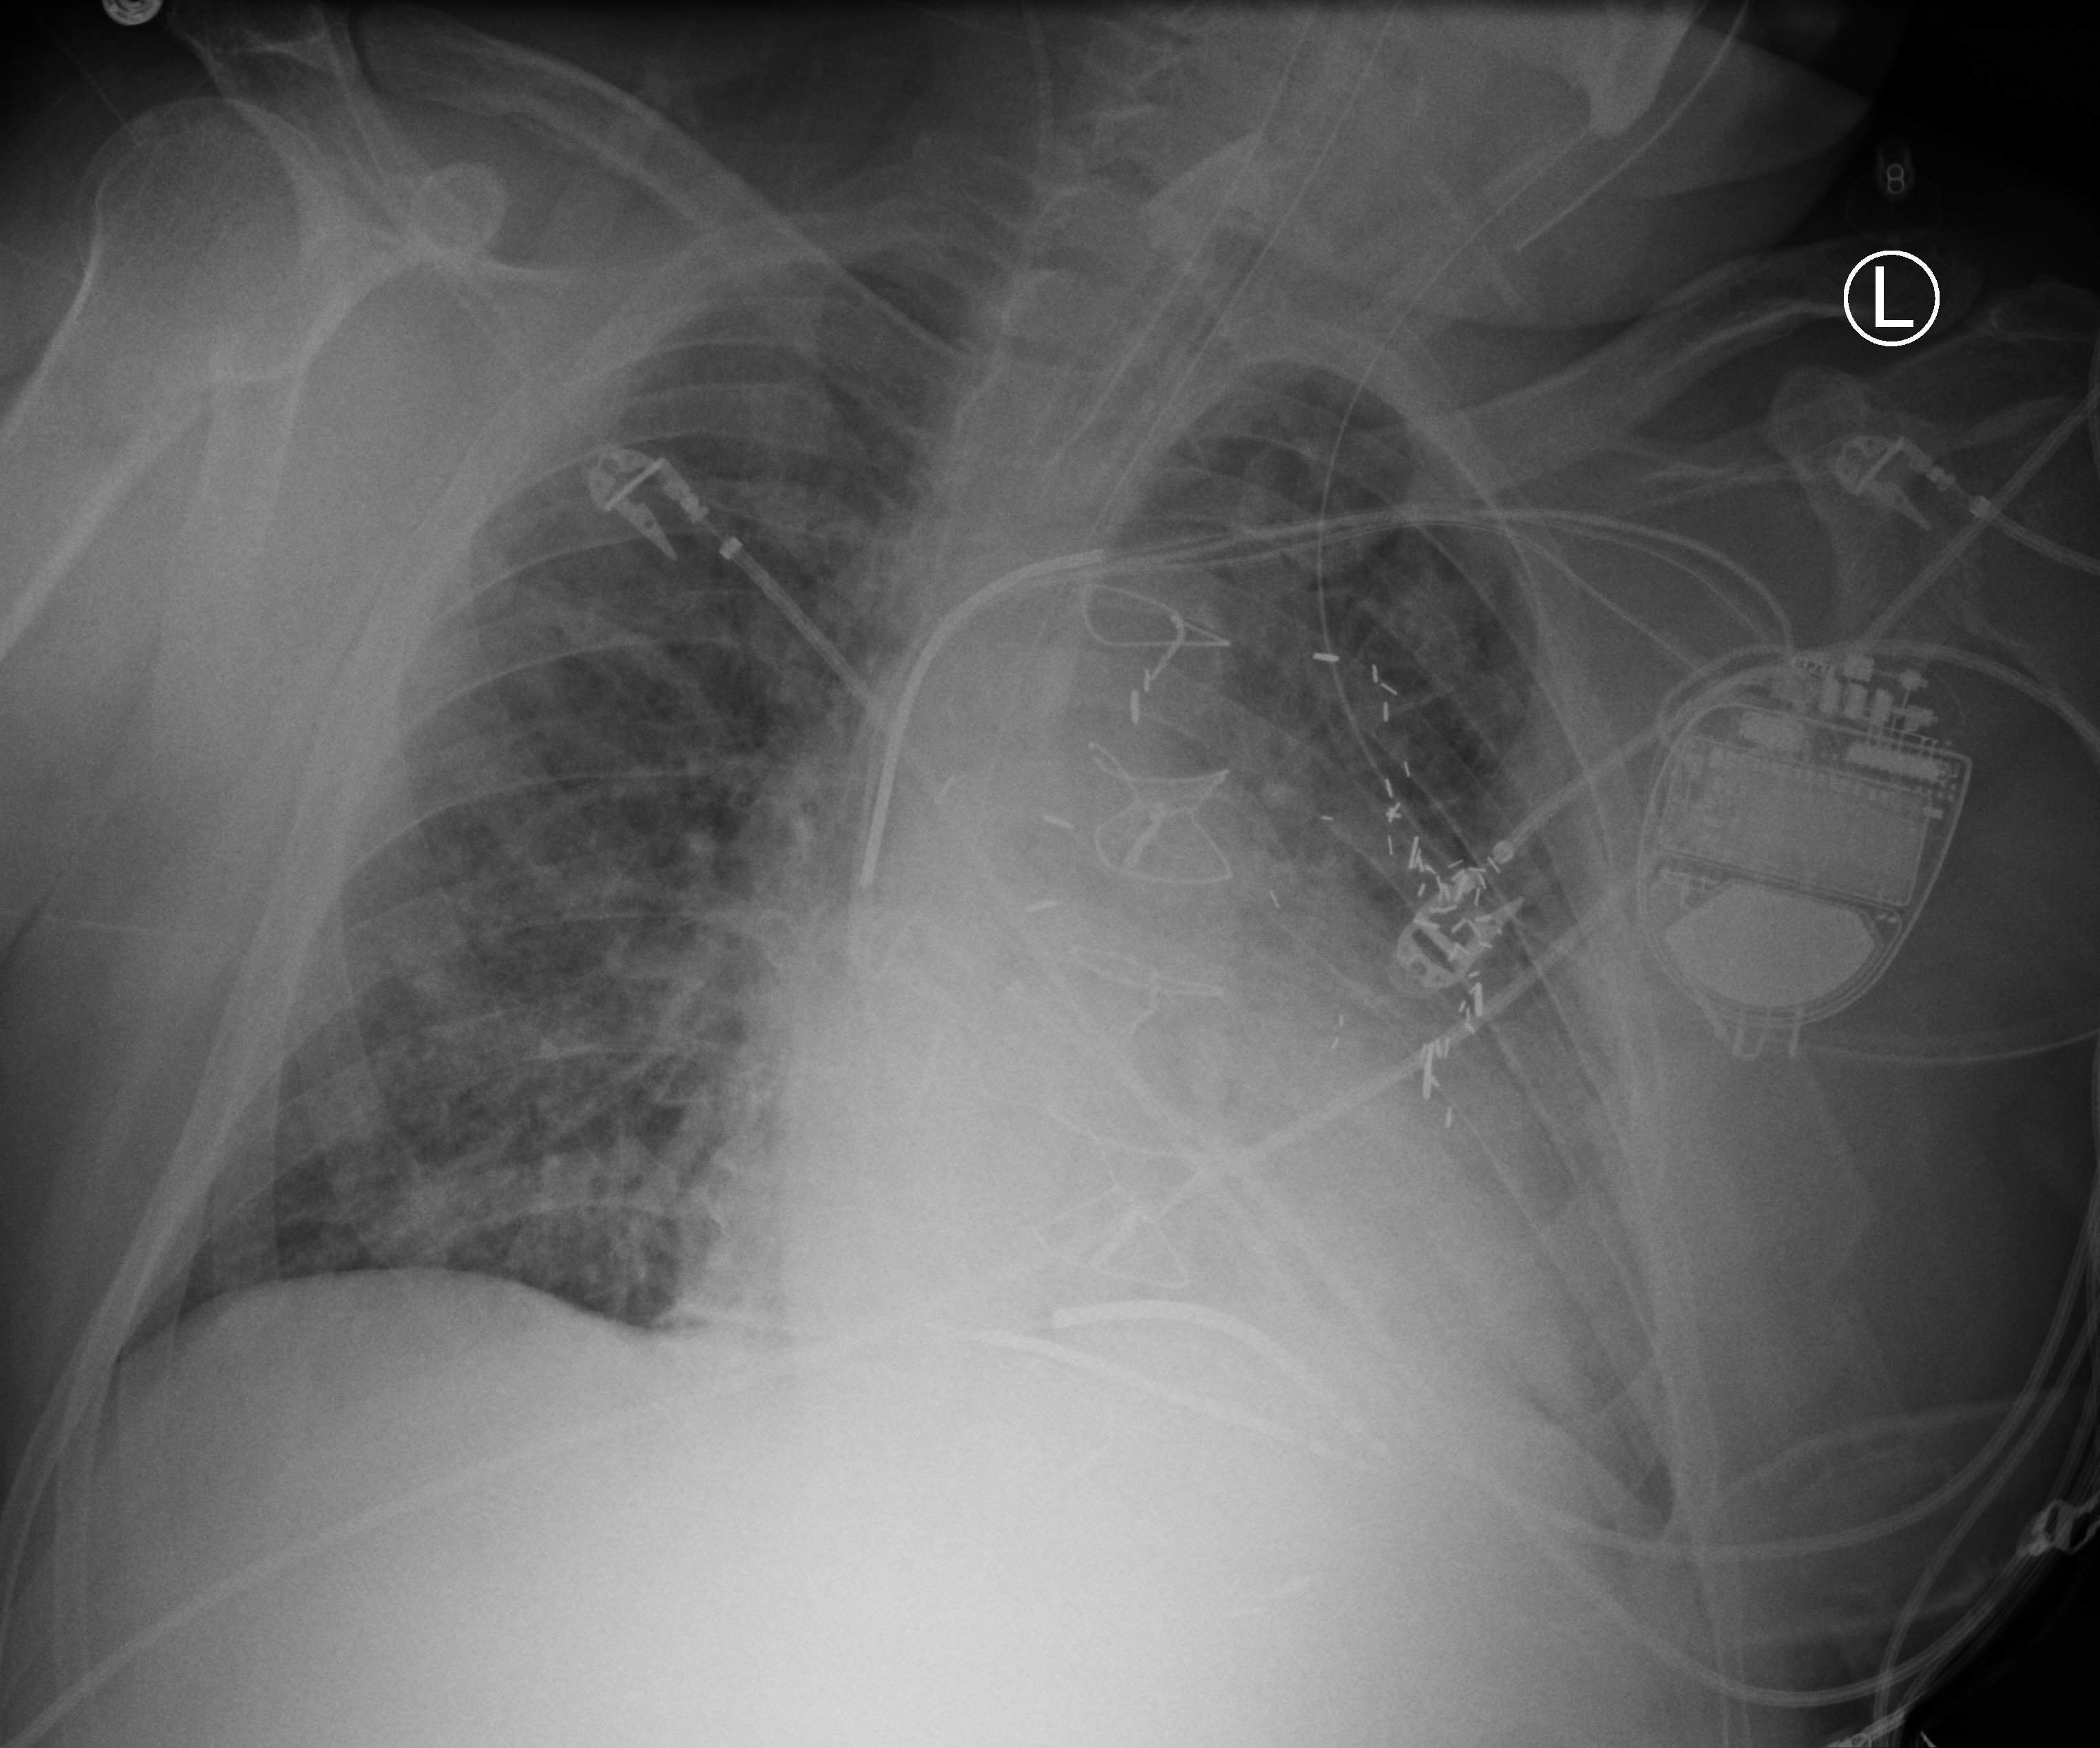
Portable chest radiograph, anteroposterior (AP) projection. Male patient hospitalised with COVID-19, age 60–74 years.
Admission-level facts for this patient (not findings on this image; timing relative to this image not recorded): length of hospital stay: 55 days.